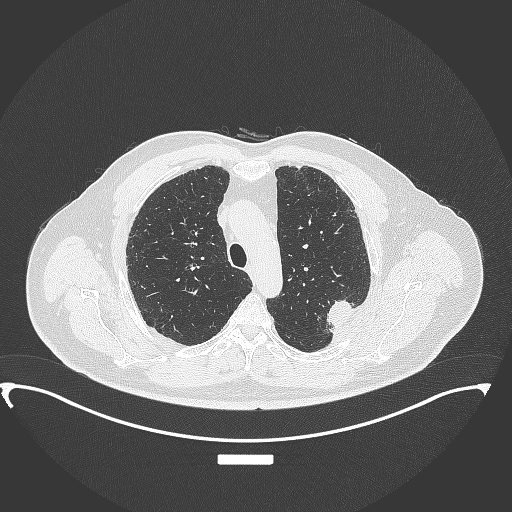
Chest CT, one axial slice. Position 271 of 350 along the scan axis. Reconstruction kernel B70f. 120 kVp. Lung window (W 1500 / L -600 HU). 1 mm slice thickness. 512 × 512 image matrix, field of view 459 × 459 mm. Patient: male, 64 years. Case-level facts recorded for this patient, not image findings: clinical TNM (as recorded): T1c N1 M1.
Outlined on this slice (rectangle marked by the reading radiologist):
- lung tumour (recorded histology: adenocarcinoma): box from (x=321, y=293) to (x=361, y=337) px